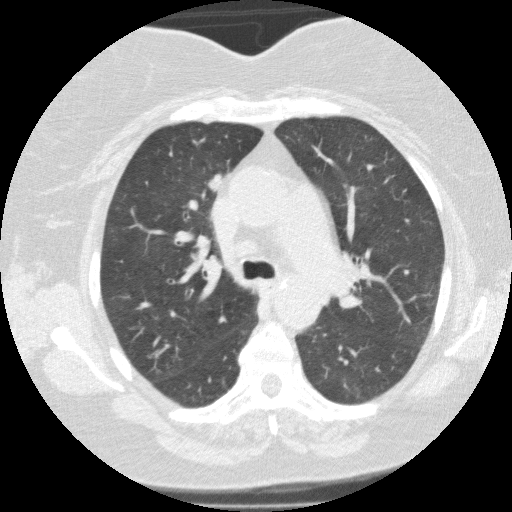
Low-dose screening chest CT, one axial slice. Slice 96 of 146 in the series (ordered by position). Lung window (W 1500 / L -600 HU). 512 × 512 image matrix, field of view 330 × 330 mm.
Outlined on this slice (outlined manually by an expert reader):
- lesion 2 (tumor, upper lobe of right lung): box from (x=206, y=173) to (x=223, y=190) px